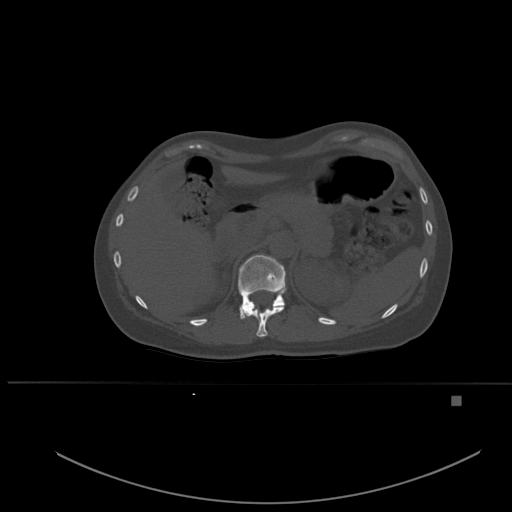
CT including the spine, one axial slice. Slice 262 of 651 in the series (ordered by position). Bone window (W 1800 / L 400 HU). 1.5 mm slice thickness. 512 × 512 image matrix, field of view 443 × 443 mm. Patient: female, 49 years. From the clinical record (not read from this slice): primary cancer: breast.
Structures marked on this image (semi-automatically segmented with operator editing):
- T11 vertebra: bounding box <244,307,284,337> (left, top, right, bottom; pixels)
- T12 vertebra: <238,255,286,320>